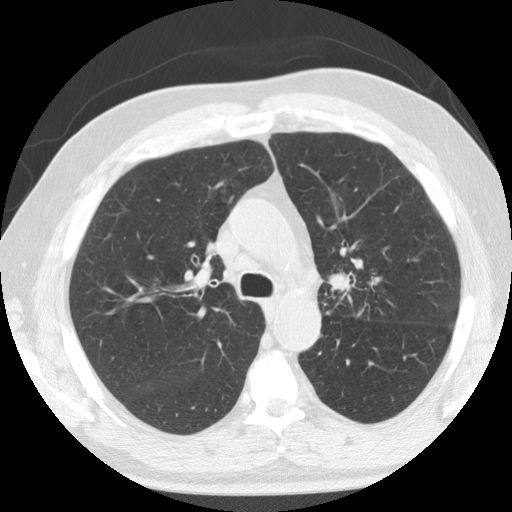
Axial slice from a low-dose chest CT screening exam; second screening round (one year after baseline); lung window (W 1500 / L -600 HU); 2.5 mm slice thickness; 512 × 512 image matrix. Male participant, aged 74 years at enrolment.
Expert reader's lesion annotation, box from (x=304, y=256) to (x=370, y=321) px. No non-calcified nodule or mass ≥4 mm was recorded by the screening reader at this exam.